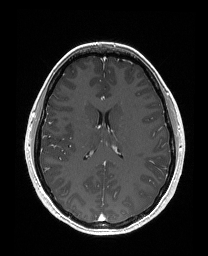
Brain MRI from a brain-tumour surgery series, one axial slice. Slice 96 of 176 in the series (ordered by position). T1-weighted post-contrast. 1 mm slice thickness. 208 × 256 image matrix, field of view 203 × 250 mm. From the clinical record (not read from this slice): histopathology: Astrocytoma; WHO grade: 3; IDH mutation: yes; tumour location: Left Frontal.
Structures marked on this image (manually delineated by an expert):
- tumour: bounding box (x1, y1, x2, y2) in pixels: (145, 134, 148, 138)